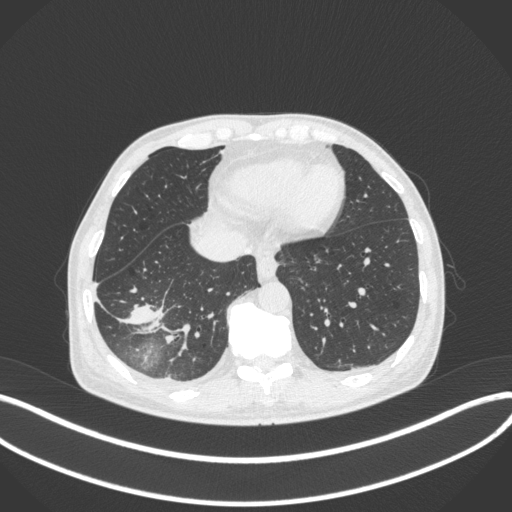
Chest CT, one axial slice. Slice 99 of 385 in the series (ordered by position). Reconstruction kernel B31f. 120 kVp. Lung window (W 1500 / L -600 HU). 1 mm slice thickness. 512 × 512 image matrix, field of view 400 × 400 mm. Patient: male, 64 years. From the clinical record (not read from this slice): clinical TNM (as recorded): T3 N0 M0.
Annotated regions visible in this slice (rectangle marked by the reading radiologist):
- lung tumour (recorded histology: adenocarcinoma): box from (x=119, y=294) to (x=165, y=344) px